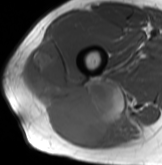
MRI of an extremity soft-tissue mass, one axial slice. Slice 59 of 61 in the series (ordered by position). MR volume resampled by the dataset authors to the PET/CT grid (not the native acquisition matrix). 3.27 mm slice thickness. 162 × 165 image matrix. Male patient. From the clinical record (not read from this slice): histological type: poorly differentiated synovial sarcoma; grade: high; site of the primary tumour: right buttock.
Structures marked on this image (expert contour drawn on MRI and transferred to this co-registered scan by the dataset authors):
- gross tumour volume including surrounding oedema: box from (x=22, y=38) to (x=138, y=146) px
- gross tumour volume (mass): (x=22, y=38)–(x=126, y=146)